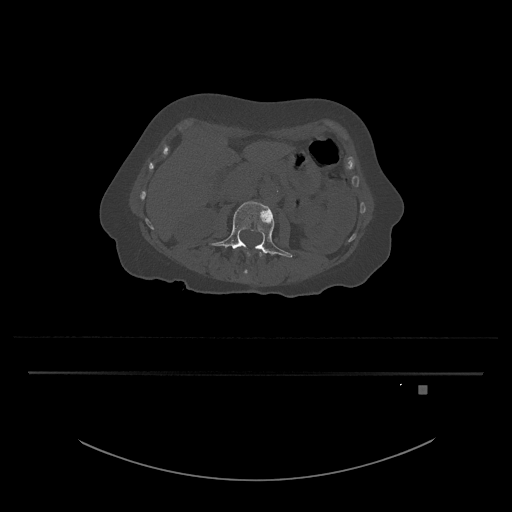
CT including the spine, one axial slice. Position 436 of 797 along the scan axis. Reconstruction kernel Br40s/3. 120 kVp. Bone window (W 1800 / L 400 HU). 512 × 512 image matrix, field of view 500 × 500 mm. Patient: female, 57 years. From the clinical record (not read from this slice): primary cancer: cervical.
Annotated regions visible in this slice (semi-automatically segmented with operator editing):
- L3 vertebra: bounding box (x1, y1, x2, y2) in pixels: (209, 201, 293, 275)